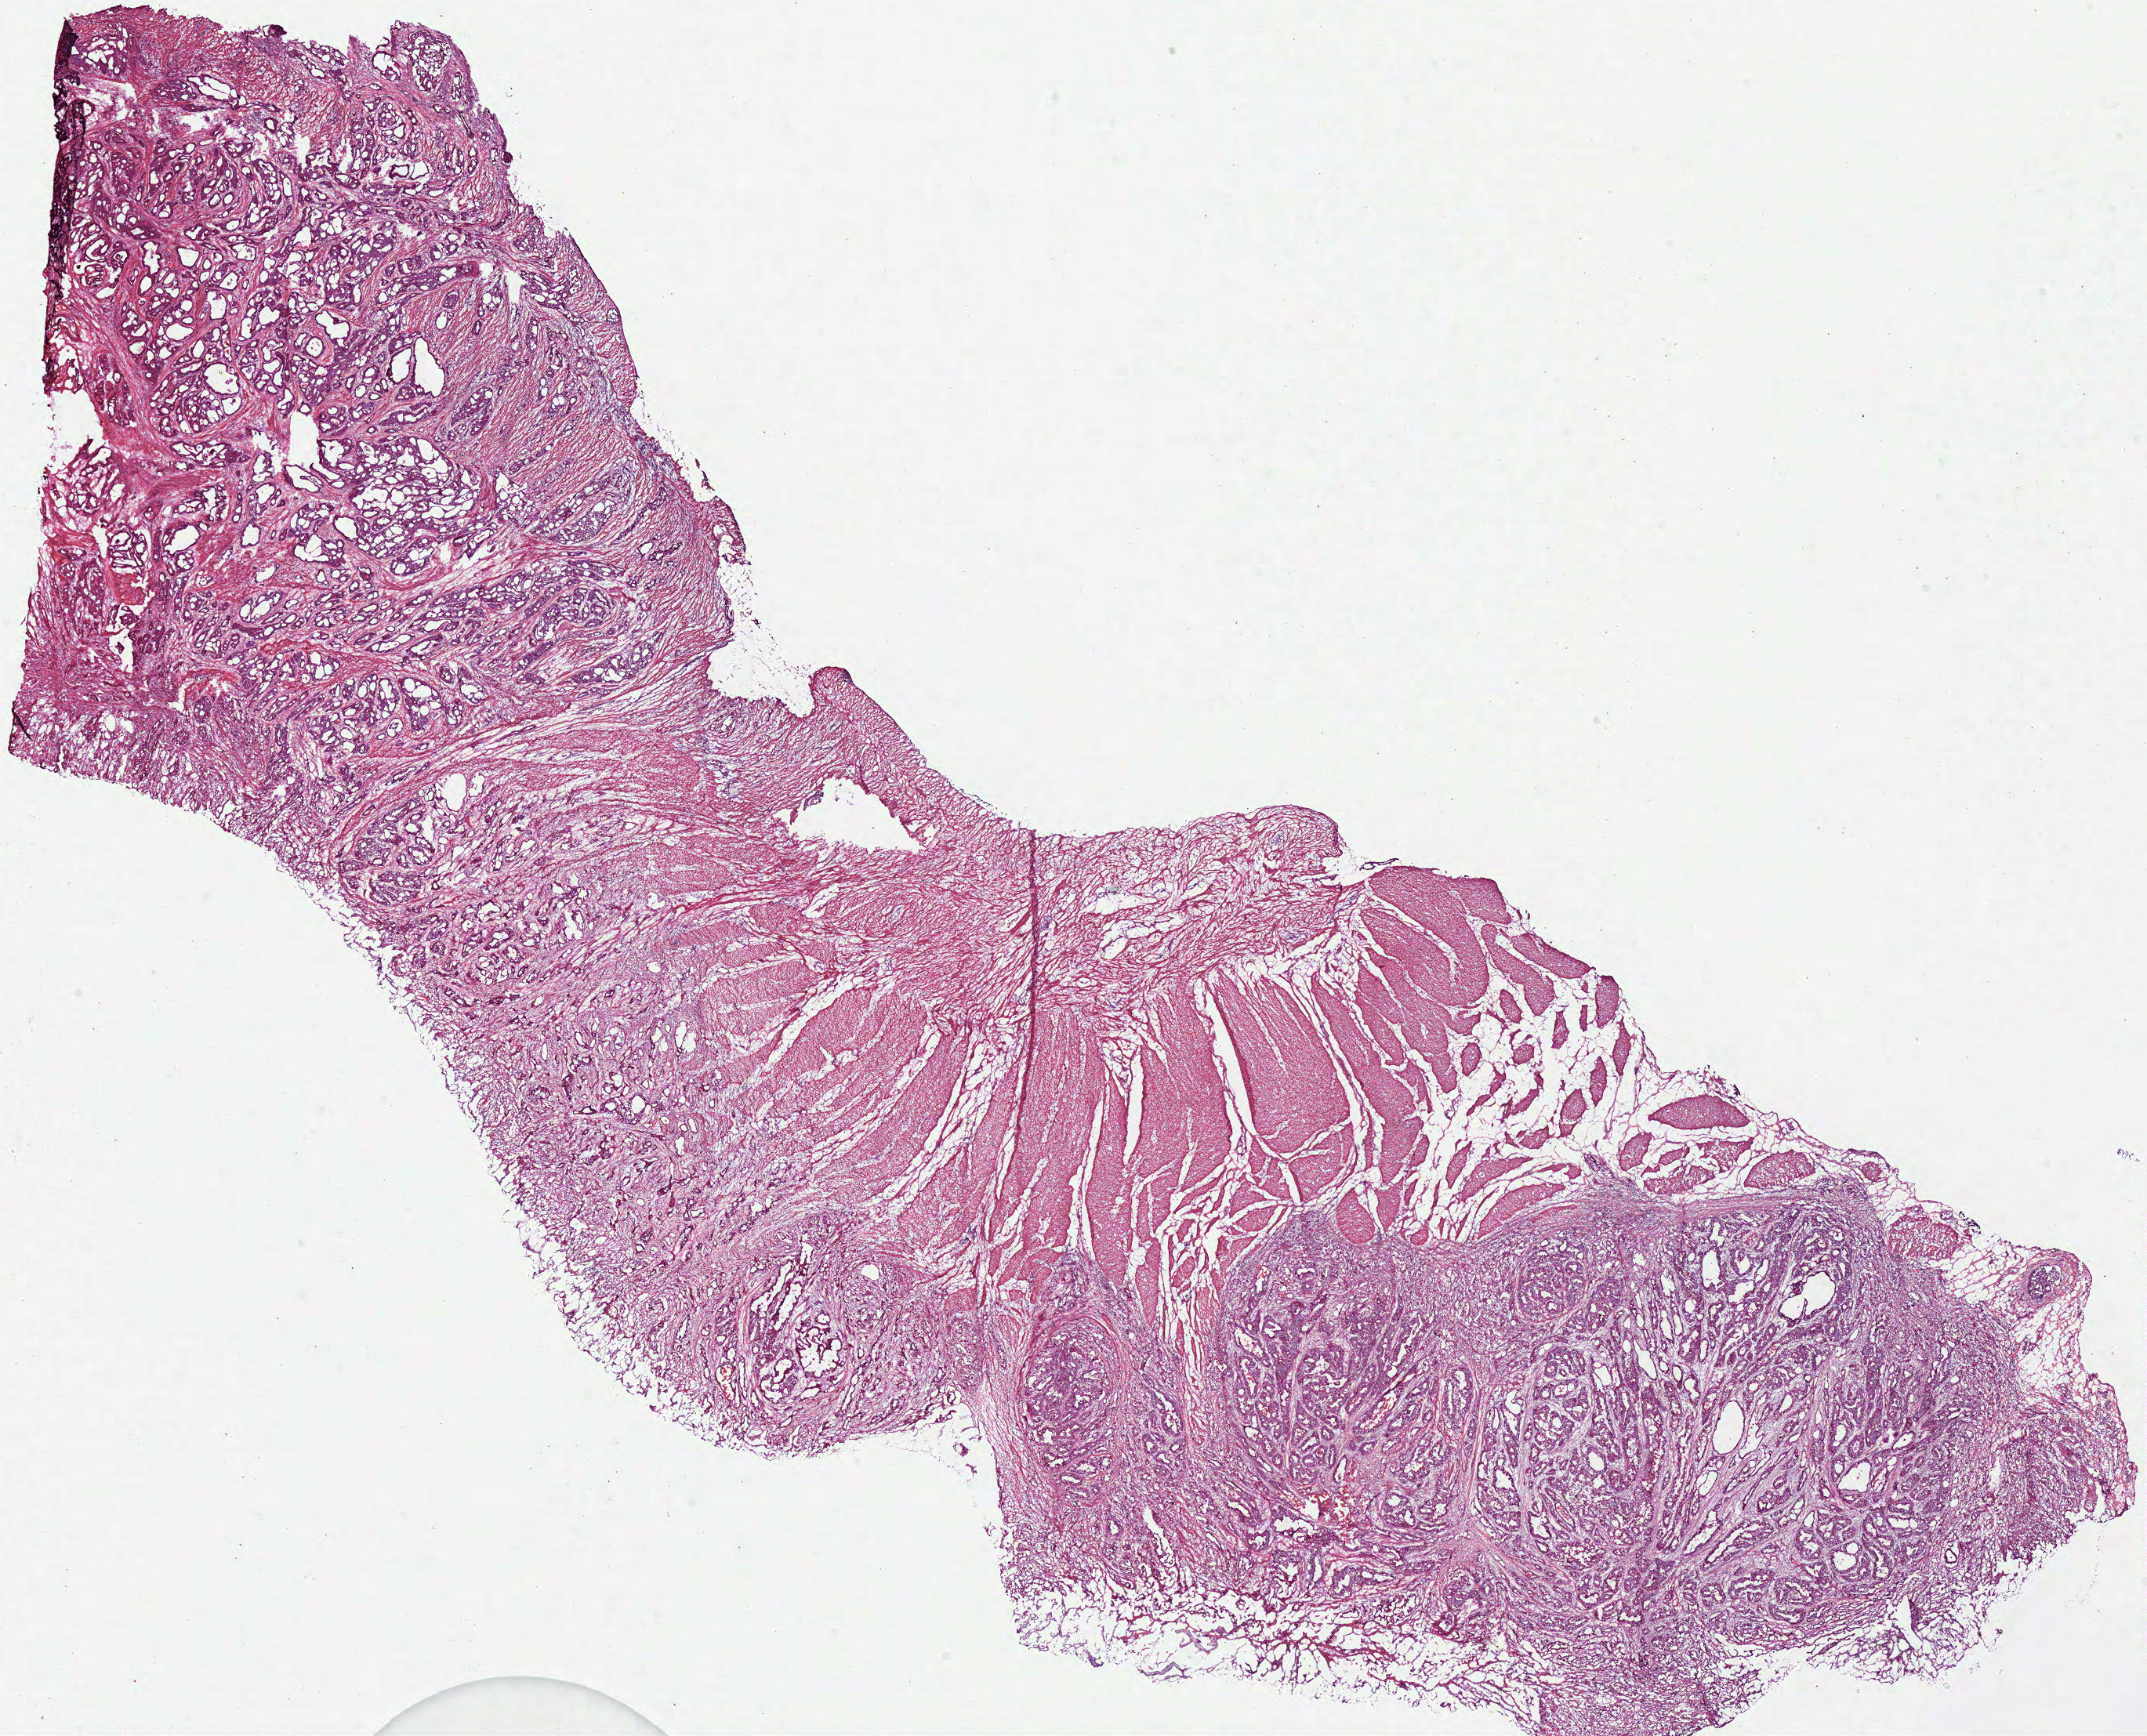
Digitized H&E tissue section (whole slide) — shown as a low-resolution overview of the whole scanned area (about 21.5 x 17.4 mm, slide scanned at 40x); frozen section; stomach, primary tumour sample. Male patient; age at initial diagnosis 70 years. Histologic grade: G2 (moderately differentiated). Pathologist review of this section (percent, as recorded): tumour cells 70%, tumour nuclei 75%, normal cells 0%, stromal cells 25%, necrosis 5%.
AJCC pathologic stage: IIA (7th edition). Diagnosis: Adenocarcinoma, NOS (body of stomach).